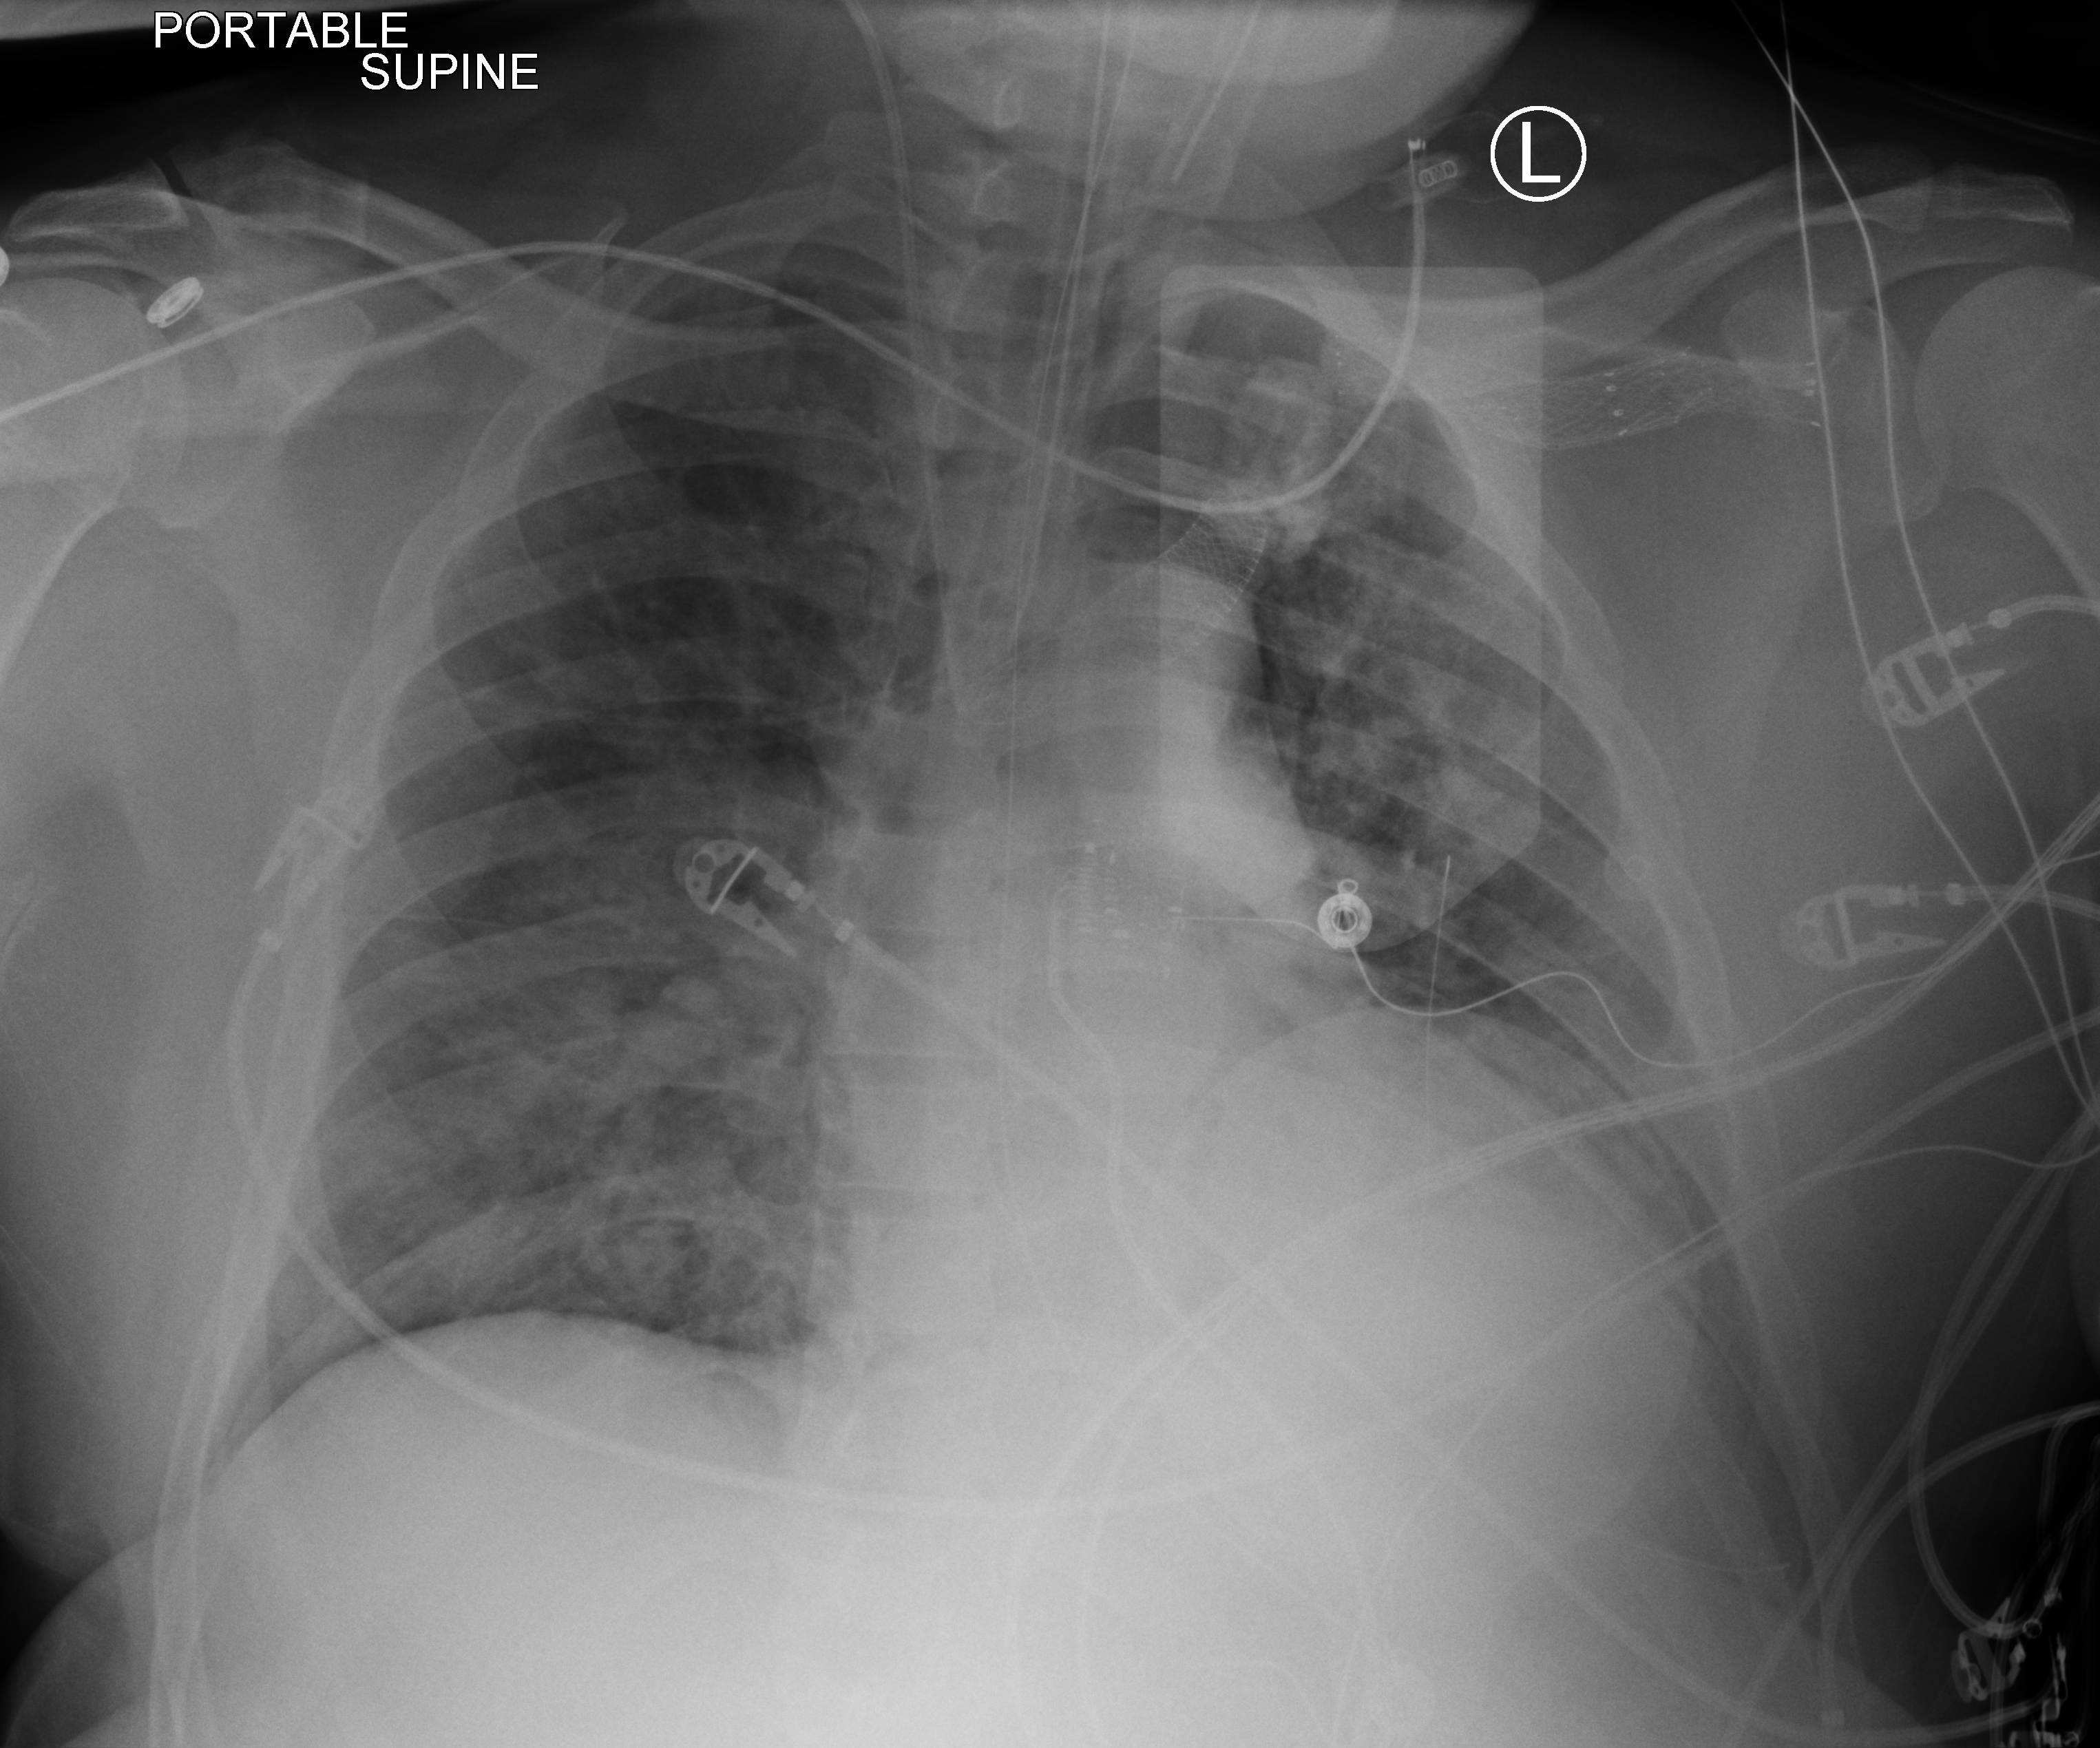
Chest X-ray (portable); anteroposterior (AP) projection. Patient hospitalised with COVID-19; male, aged 18–59 years.
From the hospital-stay record, not from the radiograph (when in the stay this image was taken is not recorded):
- admitted to intensive care during this hospital stay: yes
- mechanically ventilated during this hospital stay: yes